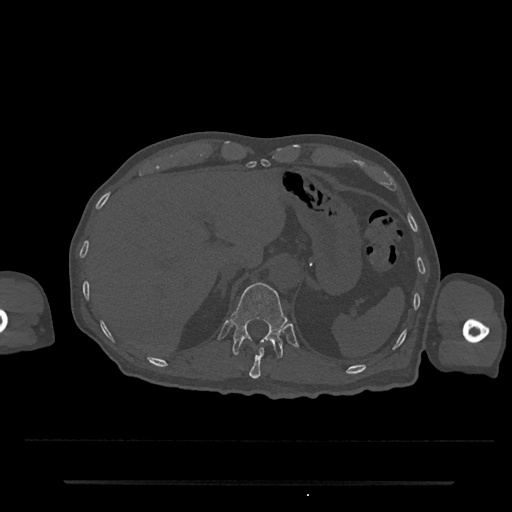
CT including the spine, one axial slice. Slice 216 of 797 in the series (ordered by position). Reconstruction kernel Br40s/3. Bone window (W 1800 / L 400 HU). 0.5 mm slice thickness. 512 × 512 image matrix. Male patient, age 74 years. From the clinical record (not read from this slice): primary cancer: prostate.
Annotated regions visible in this slice (semi-automatic segmentation, software-assisted and operator-edited):
- T11 vertebra: box from (x=249, y=347) to (x=265, y=379) px
- T12 vertebra: (x=231, y=282)–(x=288, y=358)